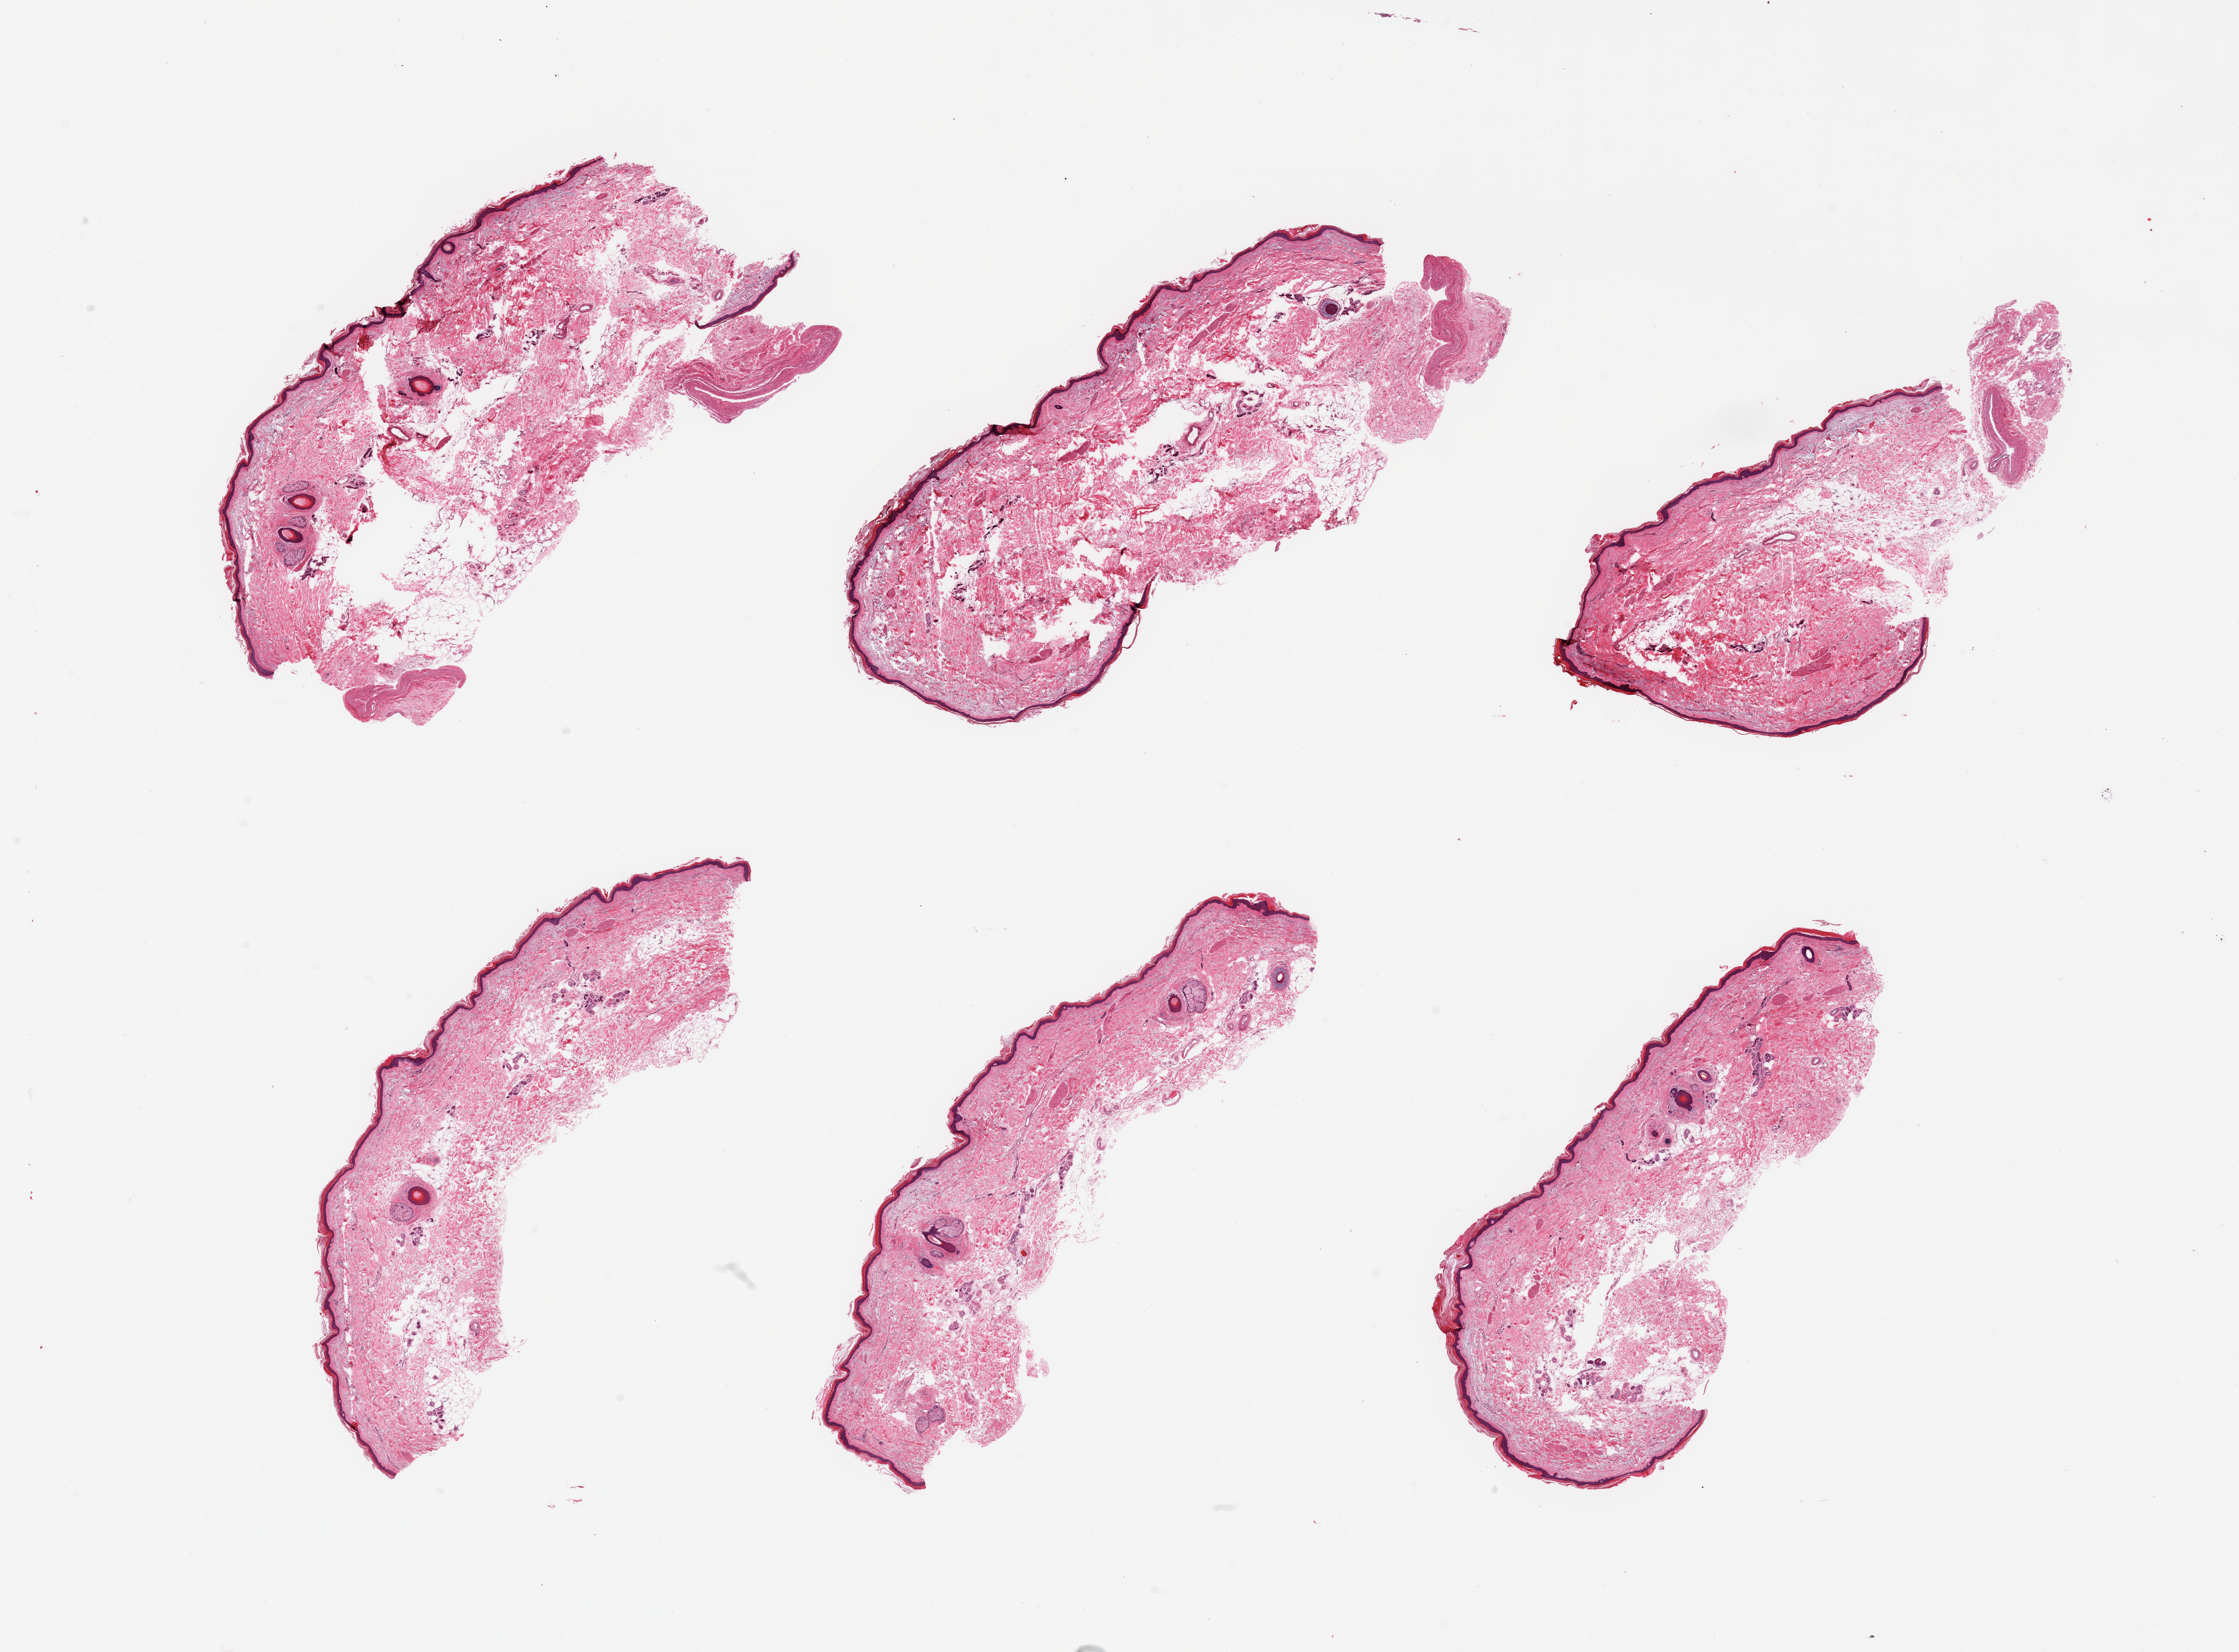
Digitized H&E-stained section — whole scanned area (about 26.6 x 19.6 mm, from a 20x scan) shown as a low-resolution overview, PAXgene-fixed paraffin-embedded (PFPE) section, sampled site (target tissue): skin of lower leg, tissue donor sample. Male donor.
* pathologist's review note for this sample: 6 pieces, moderate dermal fat, squamous epithelium 35-35 microns